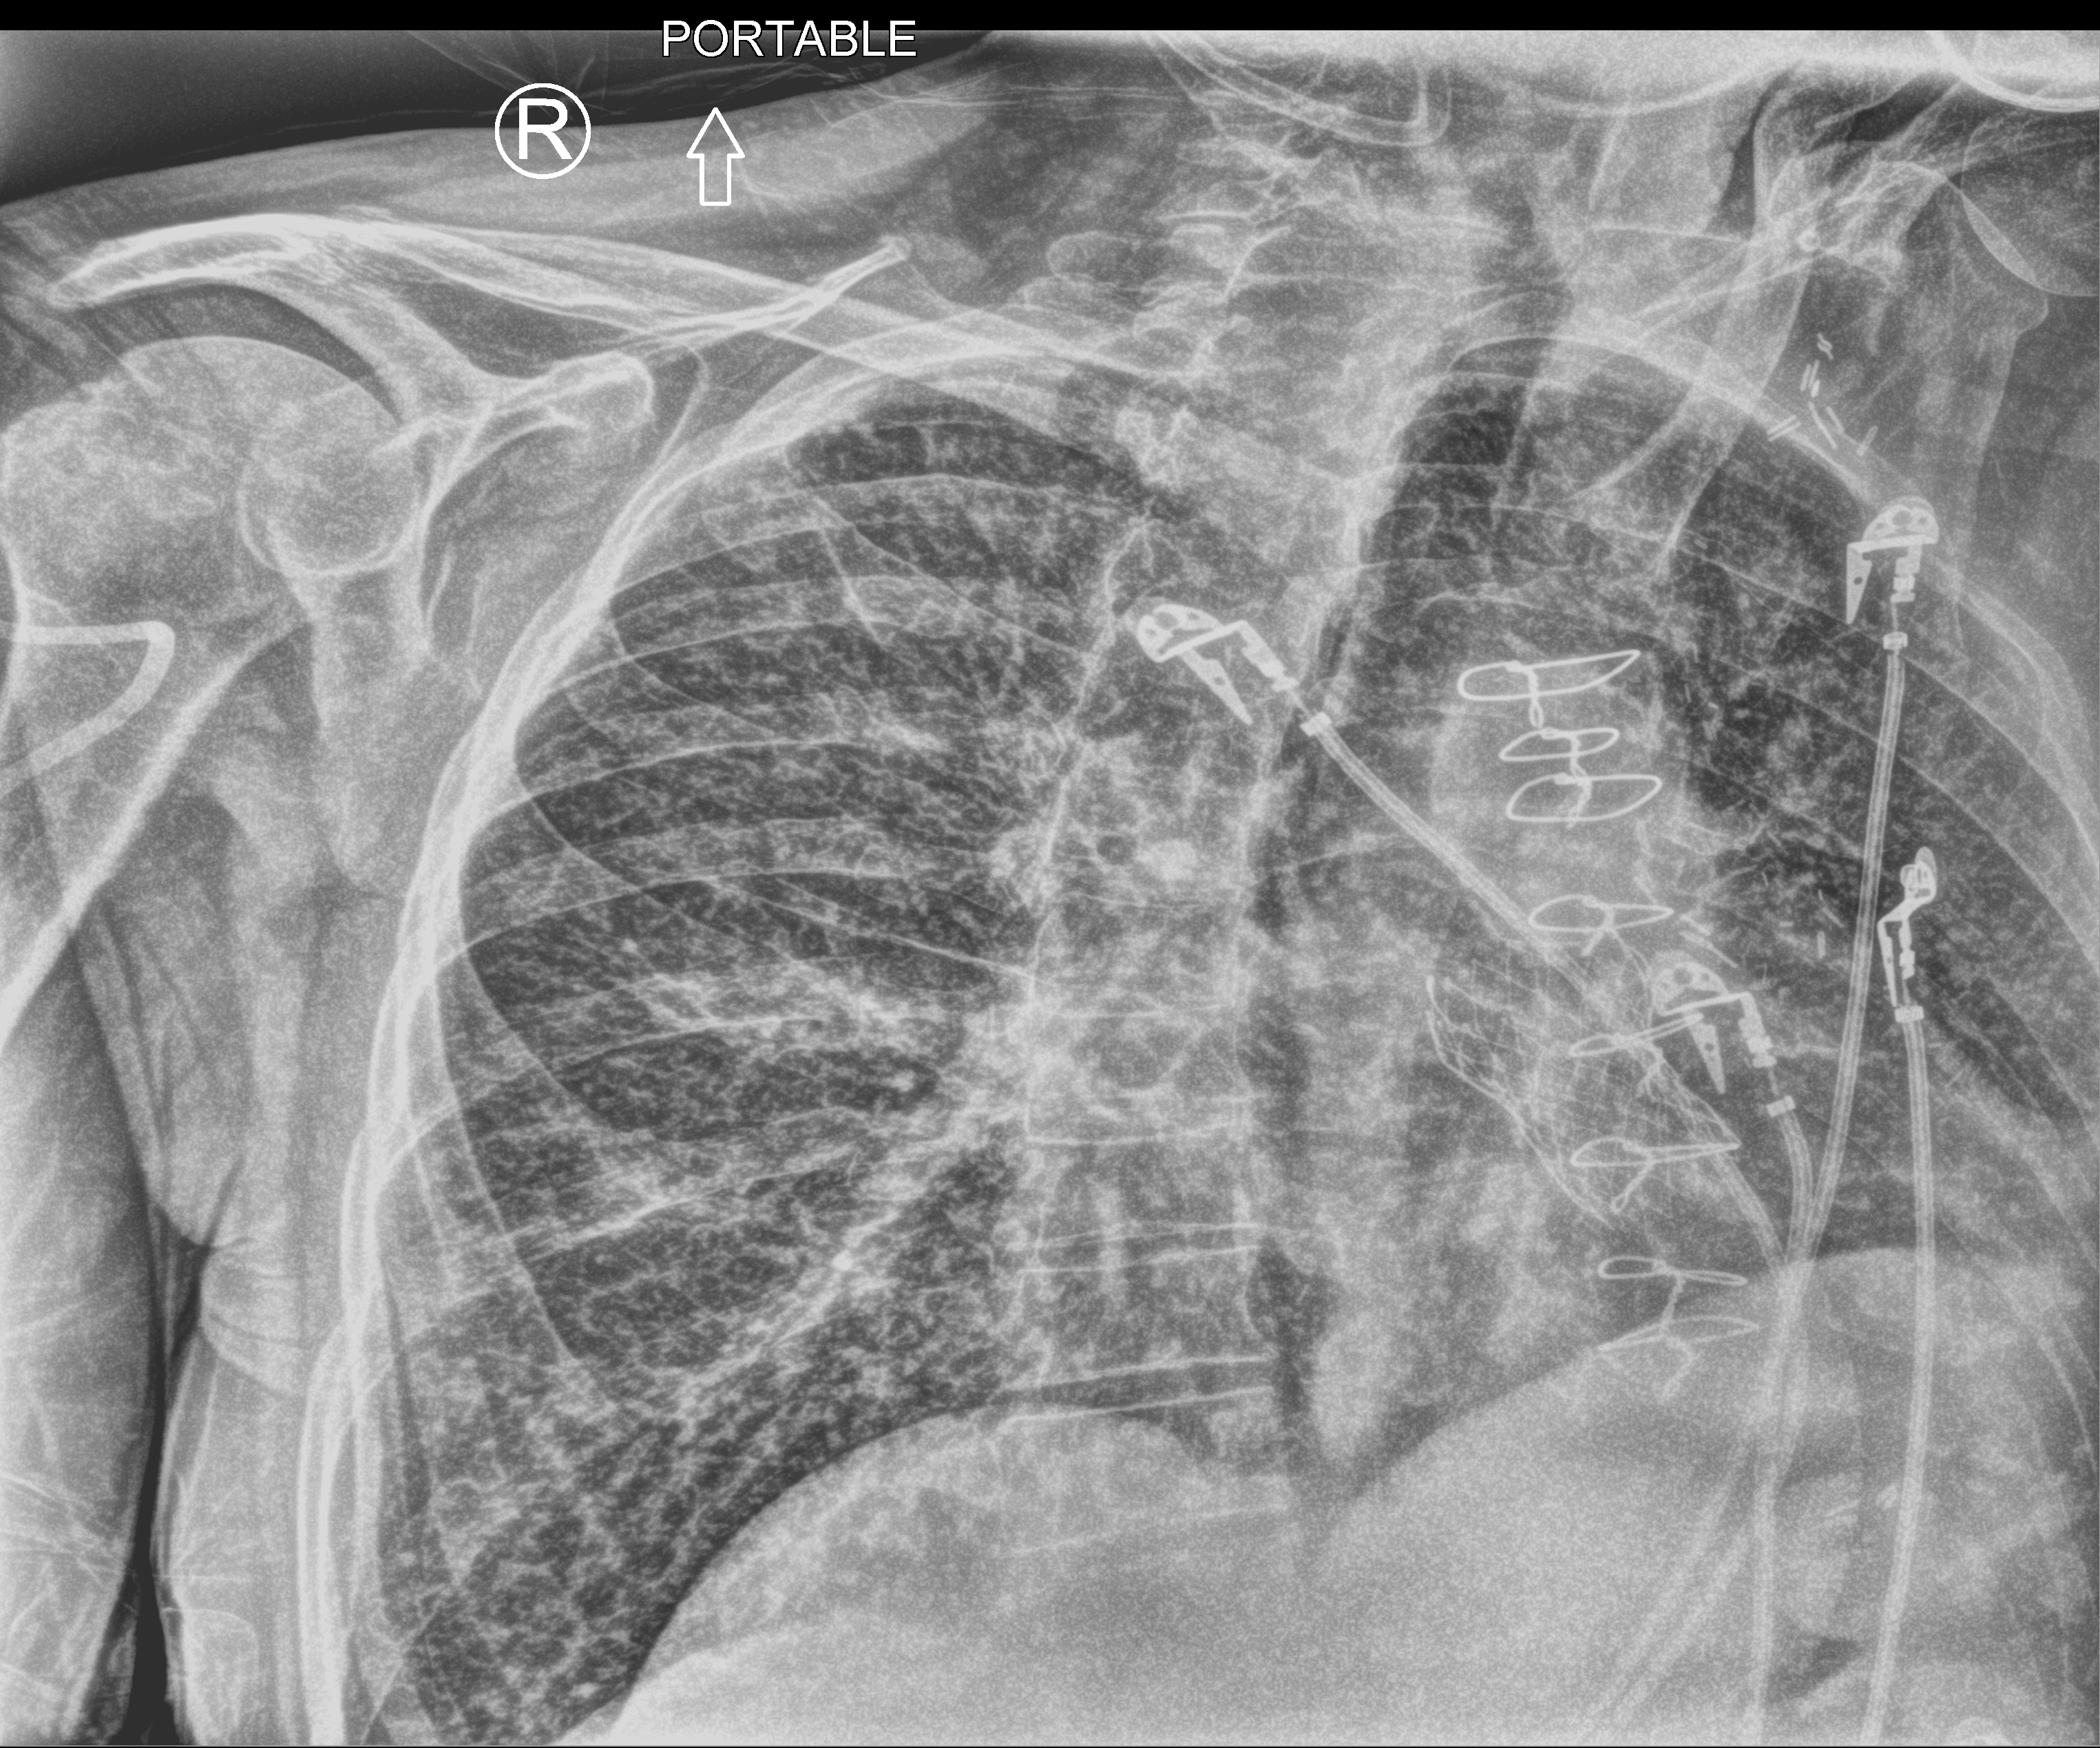
Bedside chest radiograph (computed radiography). Female patient hospitalised with COVID-19, age 75–90 years.
Hospital-stay facts (about this admission, not read from this image; timing relative to this image not recorded):
- mechanically ventilated during this hospital stay: no
- COPD (admission record): yes
- other chronic lung disease (admission record): no